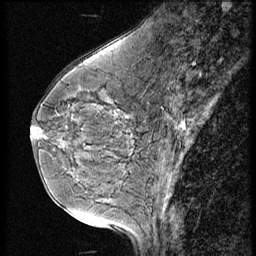
Breast MRI (dynamic contrast-enhanced), one sagittal slice; position 19 of 56 along the scan axis; 3 images stored at this slice position (order not interpretable as contrast timing); 1.5 T; TE 4.2 ms, TR 9 ms; 2.5 mm slice thickness; 256 × 256 image matrix. Patient: female, 49 years. From the clinical record (not read from this slice): setting: breast cancer imaged before/during neoadjuvant chemotherapy; receptor status: HER2-positive.
Structures marked on this image (semi-automatically segmented with operator editing):
- analysis volume of interest (the breast-tissue region the enhancement analysis was run in; not a lesion): bounding box (x1, y1, x2, y2) in pixels: (31, 75, 128, 193)
- tumour enhancement mask (voxels above the 140 % enhancement threshold inside the analysis volume of interest): (31, 130, 37, 137)